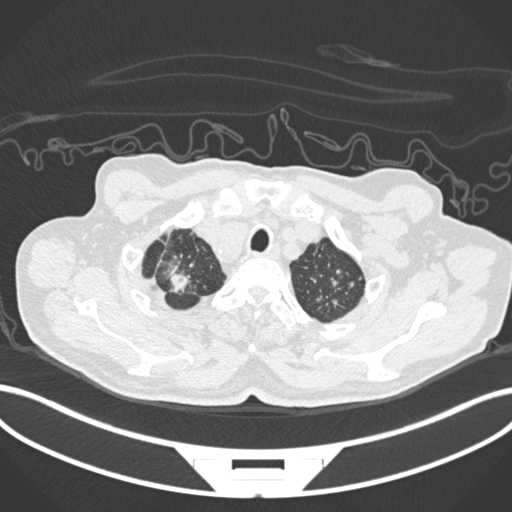
Chest CT, one axial slice. Slice 199 of 207 in the series (ordered by position). Lung window (W 1500 / L -600 HU). 1 mm slice thickness. 512 × 512 image matrix, field of view 400 × 400 mm. Patient: male, 69 years. From the clinical record (not read from this slice): clinical TNM (as recorded): T1c N1 M1.
Annotated regions visible in this slice (rectangle marked by the reading radiologist):
- lung tumour (recorded histology: adenocarcinoma): bounding box (x1, y1, x2, y2) in pixels: (166, 269, 194, 296)